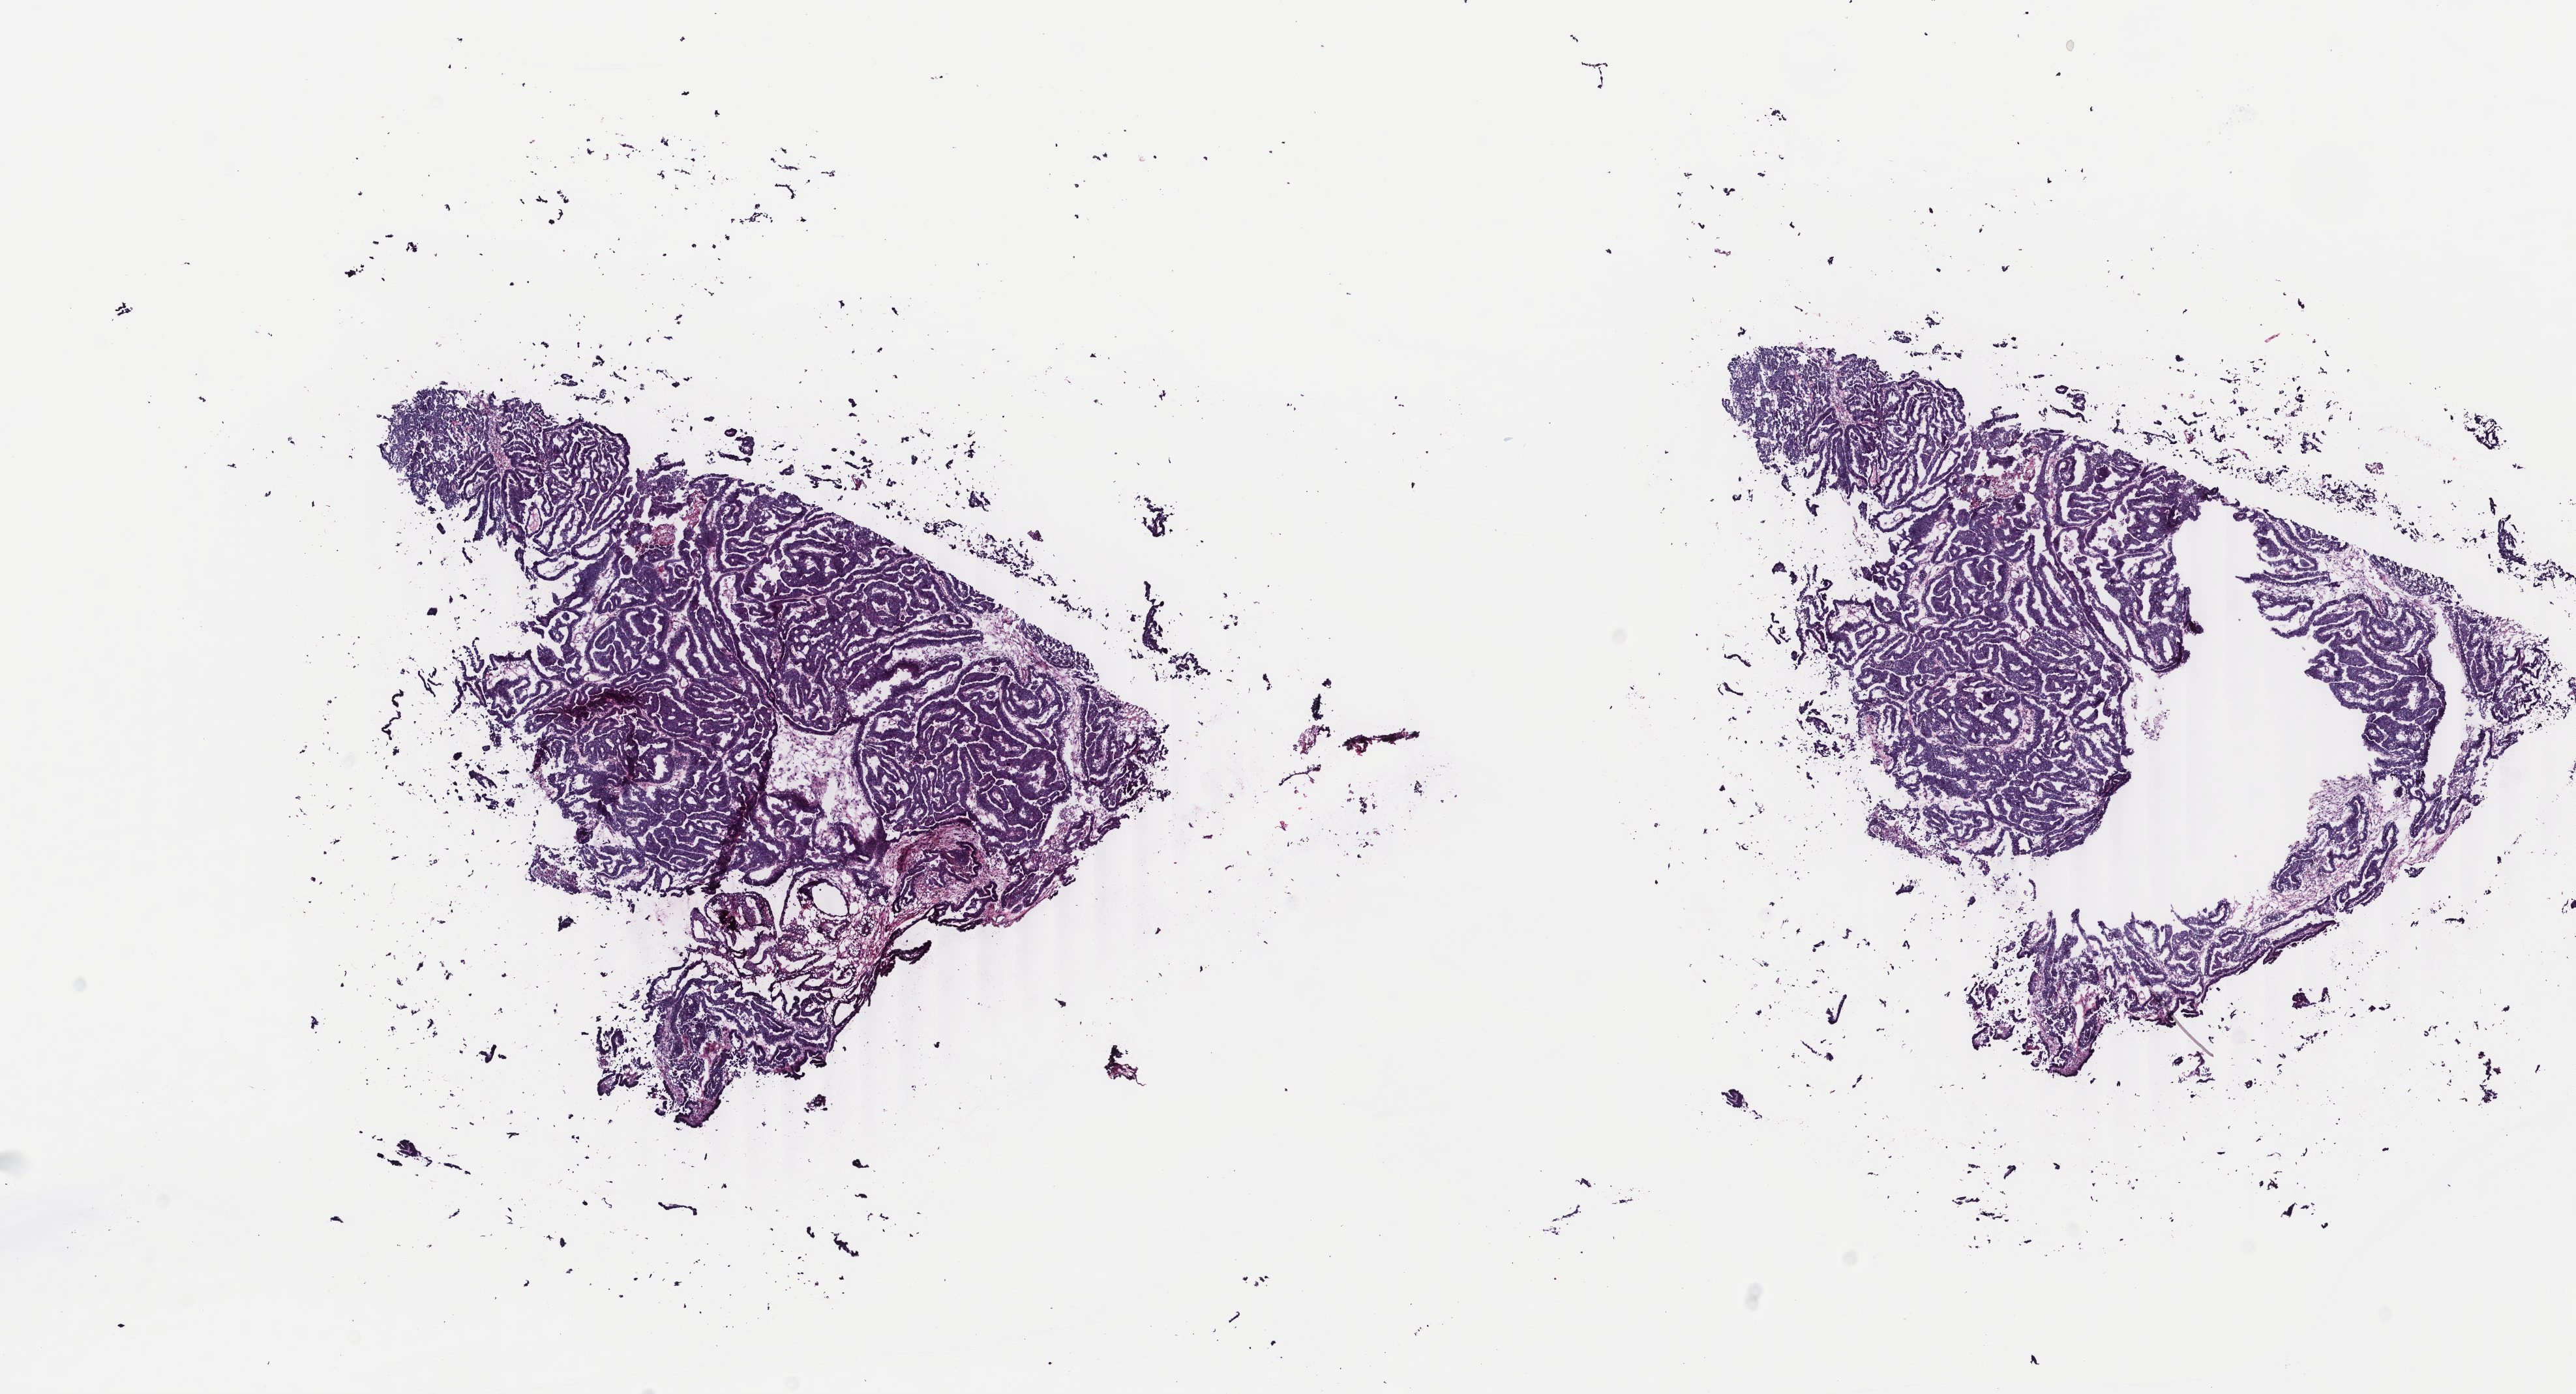
H&E whole-slide image — shown as a low-resolution overview of the whole scanned area (about 15.7 x 8.5 mm, slide scanned at 40x), frozen section from the top of the tissue portion, uterus, primary tumour sample. Female patient; age at initial diagnosis 80 years. Histologic grade: G3 (poorly differentiated). Slide review estimates, as recorded: tumour cells 100%, tumour nuclei 90%, normal cells 0%, stromal cells 0%, necrosis 0%. Inflammatory infiltration, as recorded: lymphocyte infiltration 0%, monocyte infiltration 0%, neutrophil infiltration 0%.
Histologic diagnosis: Endometrioid adenocarcinoma, NOS. FIGO stage: IB.